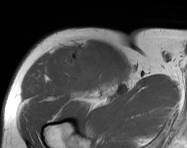
MRI of an extremity soft-tissue mass, one axial slice. Slice 105 of 114 in the series (ordered by position). MR volume resampled by the dataset authors to the PET/CT grid (not the native acquisition matrix). 3.27 mm slice thickness. 187 × 148 image matrix. Male patient. Case-level facts recorded for this patient, not image findings: histological type: pleiomorphic leiomyosarcoma; grade: intermediate; site of the primary tumour: right thigh.
Annotated regions visible in this slice (expert contour drawn on MRI and transferred to this co-registered scan by the dataset authors):
- gross tumour volume including surrounding oedema: bounding box (x1, y1, x2, y2) in pixels: (61, 41, 122, 96)
- gross tumour volume (mass): (66, 50, 121, 94)